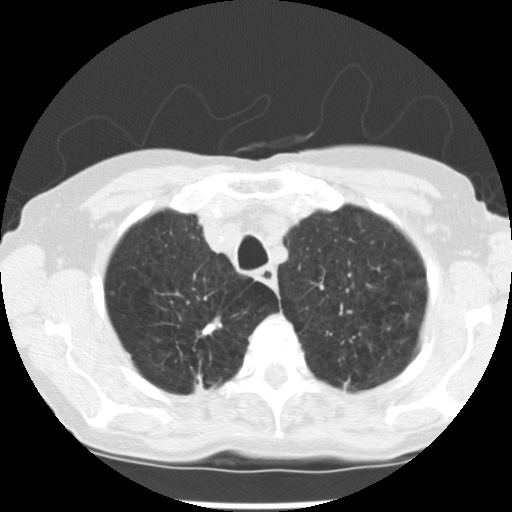
Axial slice from a low-dose chest CT screening exam. First (baseline) screen. Lung window (W 1500 / L -600 HU). 2.5 mm slice thickness. Standard (soft-tissue) reconstruction kernel (STANDARD). Female, age 72 years at enrolment.
Lesion marked by an expert reader, bounding box [x1, y1, x2, y2] px = [184, 310, 231, 347]. The screening reader recorded 3 non-calcified nodules or masses ≥4 mm on this exam (right upper lobe, left upper lobe, left lower lobe); which of them this box marks is not recorded. Official screen result: positive, change unspecified: nodule(s) >= 4 mm or enlarging nodule(s), mass(es), or other non-specific abnormalities suspicious for lung cancer. Later outcome: lung cancer diagnosed 50 days after this screen — adenocarcinoma, NOS, right upper lobe, moderately differentiated (G2), stage IB (AJCC 6th edition), 22 mm at pathology.